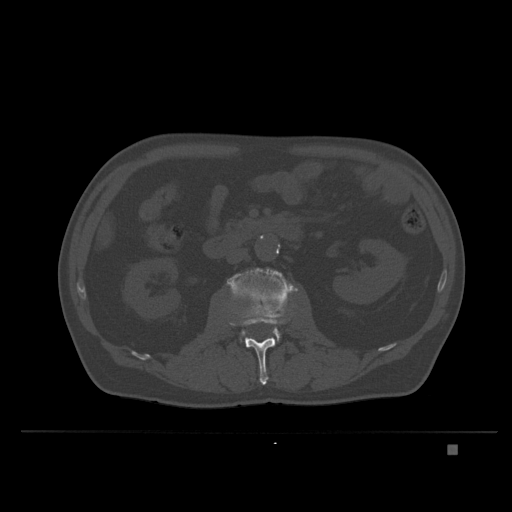
CT including the spine, one axial slice; position 110 of 435 along the scan axis; bone window (W 1800 / L 400 HU); 512 × 512 image matrix. Patient: male, 73 years. From the clinical record (not read from this slice): primary cancer: skin.
Outlined on this slice (semi-automatically segmented with operator editing):
- L2 vertebra: bounding box (x1, y1, x2, y2) in pixels: (229, 316, 287, 385)
- L3 vertebra: (227, 267, 298, 341)